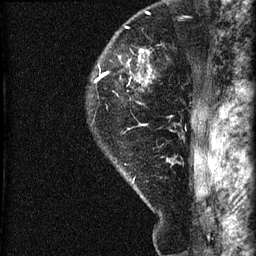
Breast MRI (dynamic contrast-enhanced), one sagittal slice; position 53 of 60 along the scan axis; dynamic contrast-enhanced series, image 2 of 3 at this slice position (ordered by acquisition); 1.5 T; TE 4.2 ms, TR 22.7 ms; 1.8 mm slice thickness; 256 × 256 image matrix. Female patient, age 45 years. Case-level facts recorded for this patient, not image findings: setting: breast cancer imaged before/during neoadjuvant chemotherapy; receptor status: HR-positive, HER2-negative.
Annotated regions visible in this slice (semi-automatic segmentation, software-assisted and operator-edited):
- analysis volume of interest (the breast-tissue region the enhancement analysis was run in; not a lesion): bounding box (x1, y1, x2, y2) in pixels: (86, 11, 205, 140)
- tumour enhancement mask (voxels above the 90 % enhancement threshold inside the analysis volume of interest): (97, 53, 151, 80)